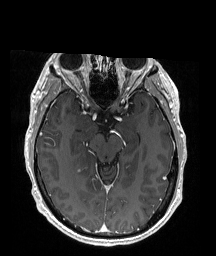
Brain MRI from a brain-tumour surgery series, one axial slice. Position 113 of 176 along the scan axis. T1-weighted post-contrast. 1 mm slice thickness. 216 × 256 image matrix, field of view 211 × 250 mm. From the clinical record (not read from this slice): histopathology: Oligodendroglioma; WHO grade: 2; IDH mutation: yes; tumour location: Right Parietal.
Outlined on this slice (manually delineated by an expert):
- tumour: bounding box [x1, y1, x2, y2] px = [74, 150, 95, 205]